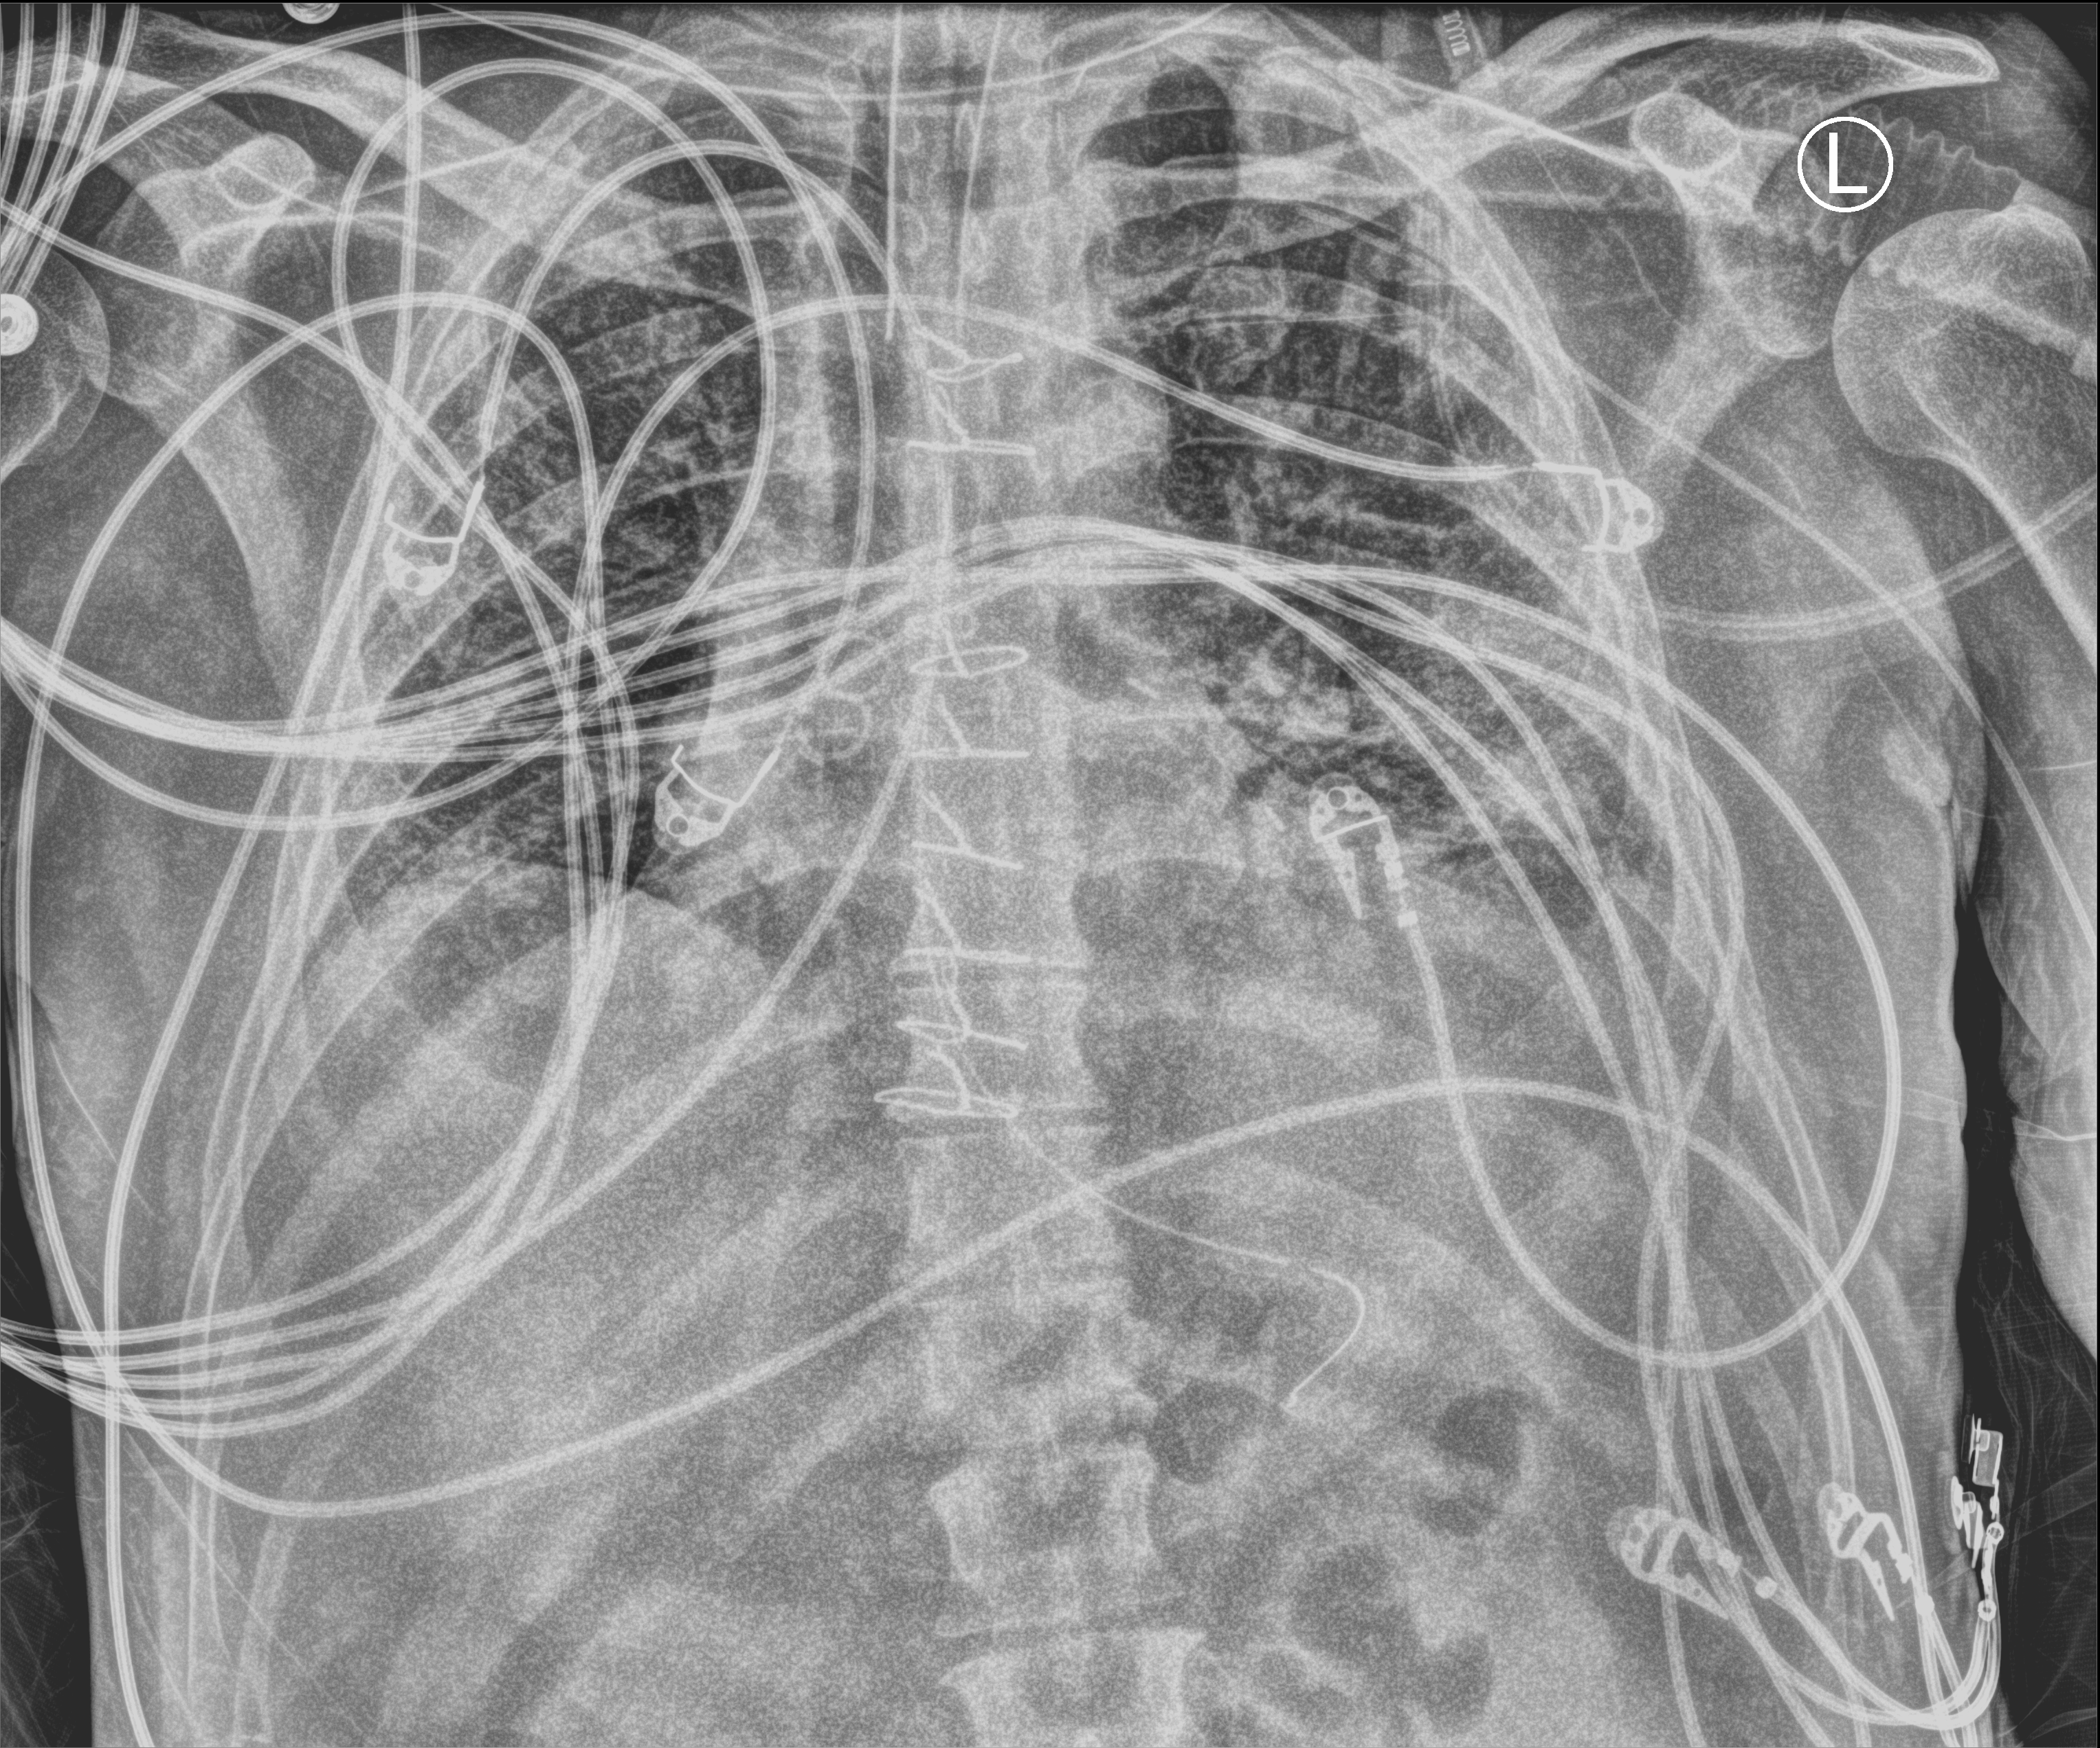
Chest X-ray (portable), anteroposterior (AP) projection. Male patient hospitalised with COVID-19, age 18–59 years.
From the hospital-stay record, not from the radiograph (when in the stay this image was taken is not recorded):
- admitted to intensive care during this hospital stay: yes
- COPD (admission record): yes
- mechanically ventilated during this hospital stay: yes